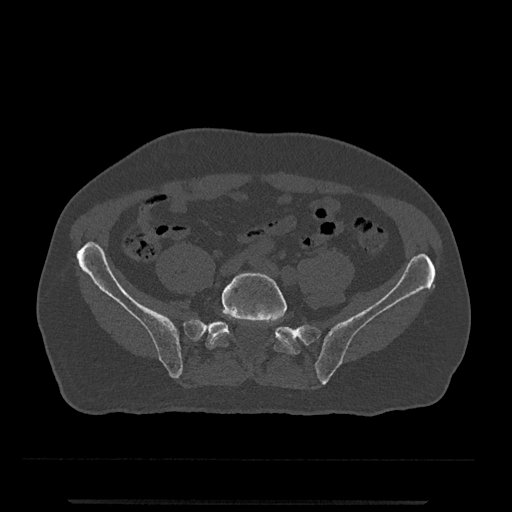
CT including the spine, one axial slice; position 48 of 797 along the scan axis; reconstruction kernel Br40s/3; 120 kVp; bone window (W 1800 / L 400 HU); 512 × 512 image matrix. Patient: male, 63 years. Case-level facts recorded for this patient, not image findings: primary cancer: prostate.
Annotated regions visible in this slice (semi-automatic segmentation, software-assisted and operator-edited):
- L5 vertebra: bounding box [x1, y1, x2, y2] px = [209, 272, 293, 354]